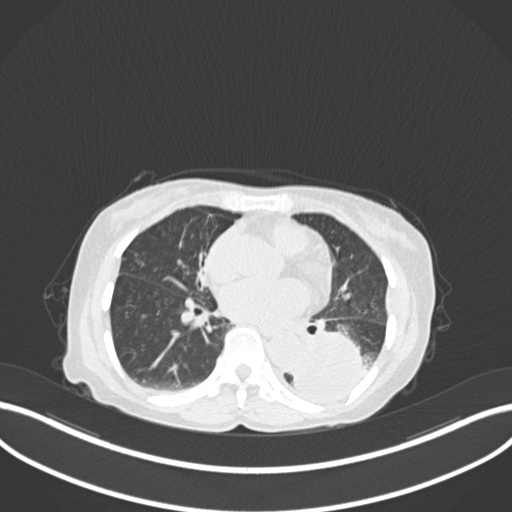
Chest CT, one axial slice. Position 64 of 233 along the scan axis. 120 kVp. Lung window (W 1500 / L -600 HU). 512 × 512 image matrix. Patient: female, 78 years. Case-level facts recorded for this patient, not image findings: clinical TNM (as recorded): T3 N0 M1.
Structures marked on this image (rectangle marked by the reading radiologist):
- lung tumour (recorded histology: squamous cell carcinoma): box from (x=289, y=325) to (x=369, y=407) px